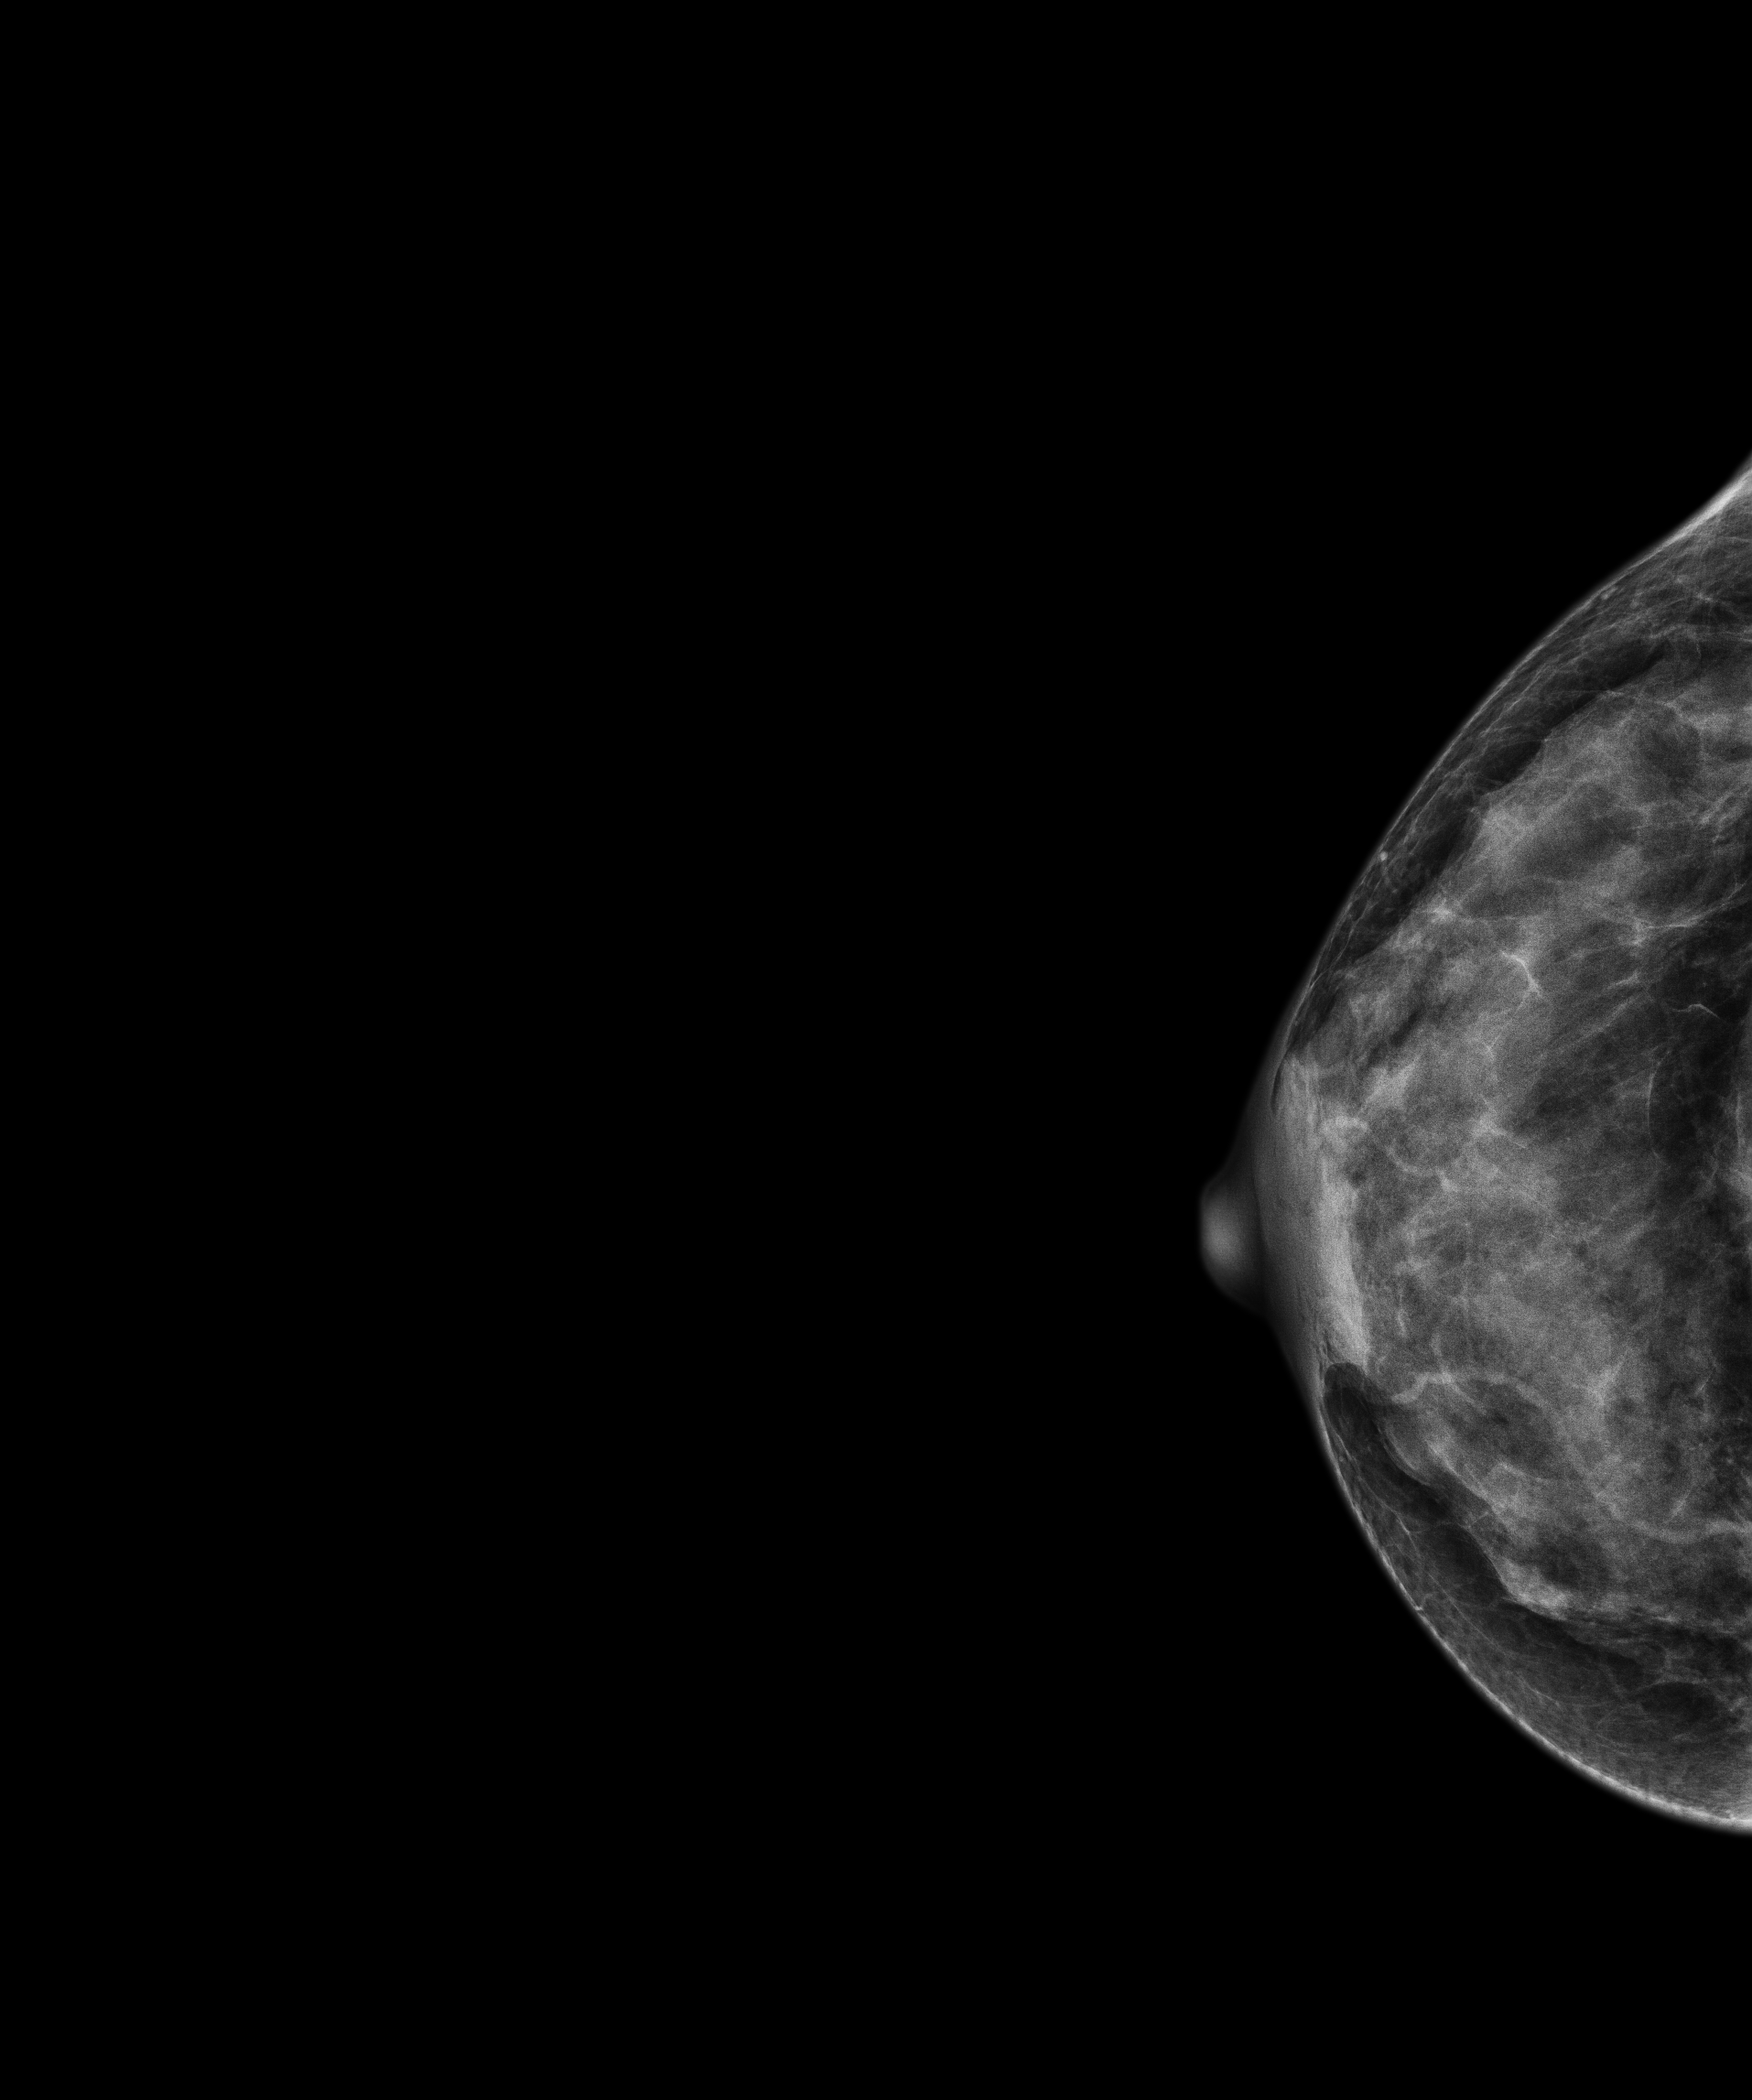
Screening examination. Female patient, age 47 years.
Image type: full-field digital mammogram. Breast: right. Projection: CC view.